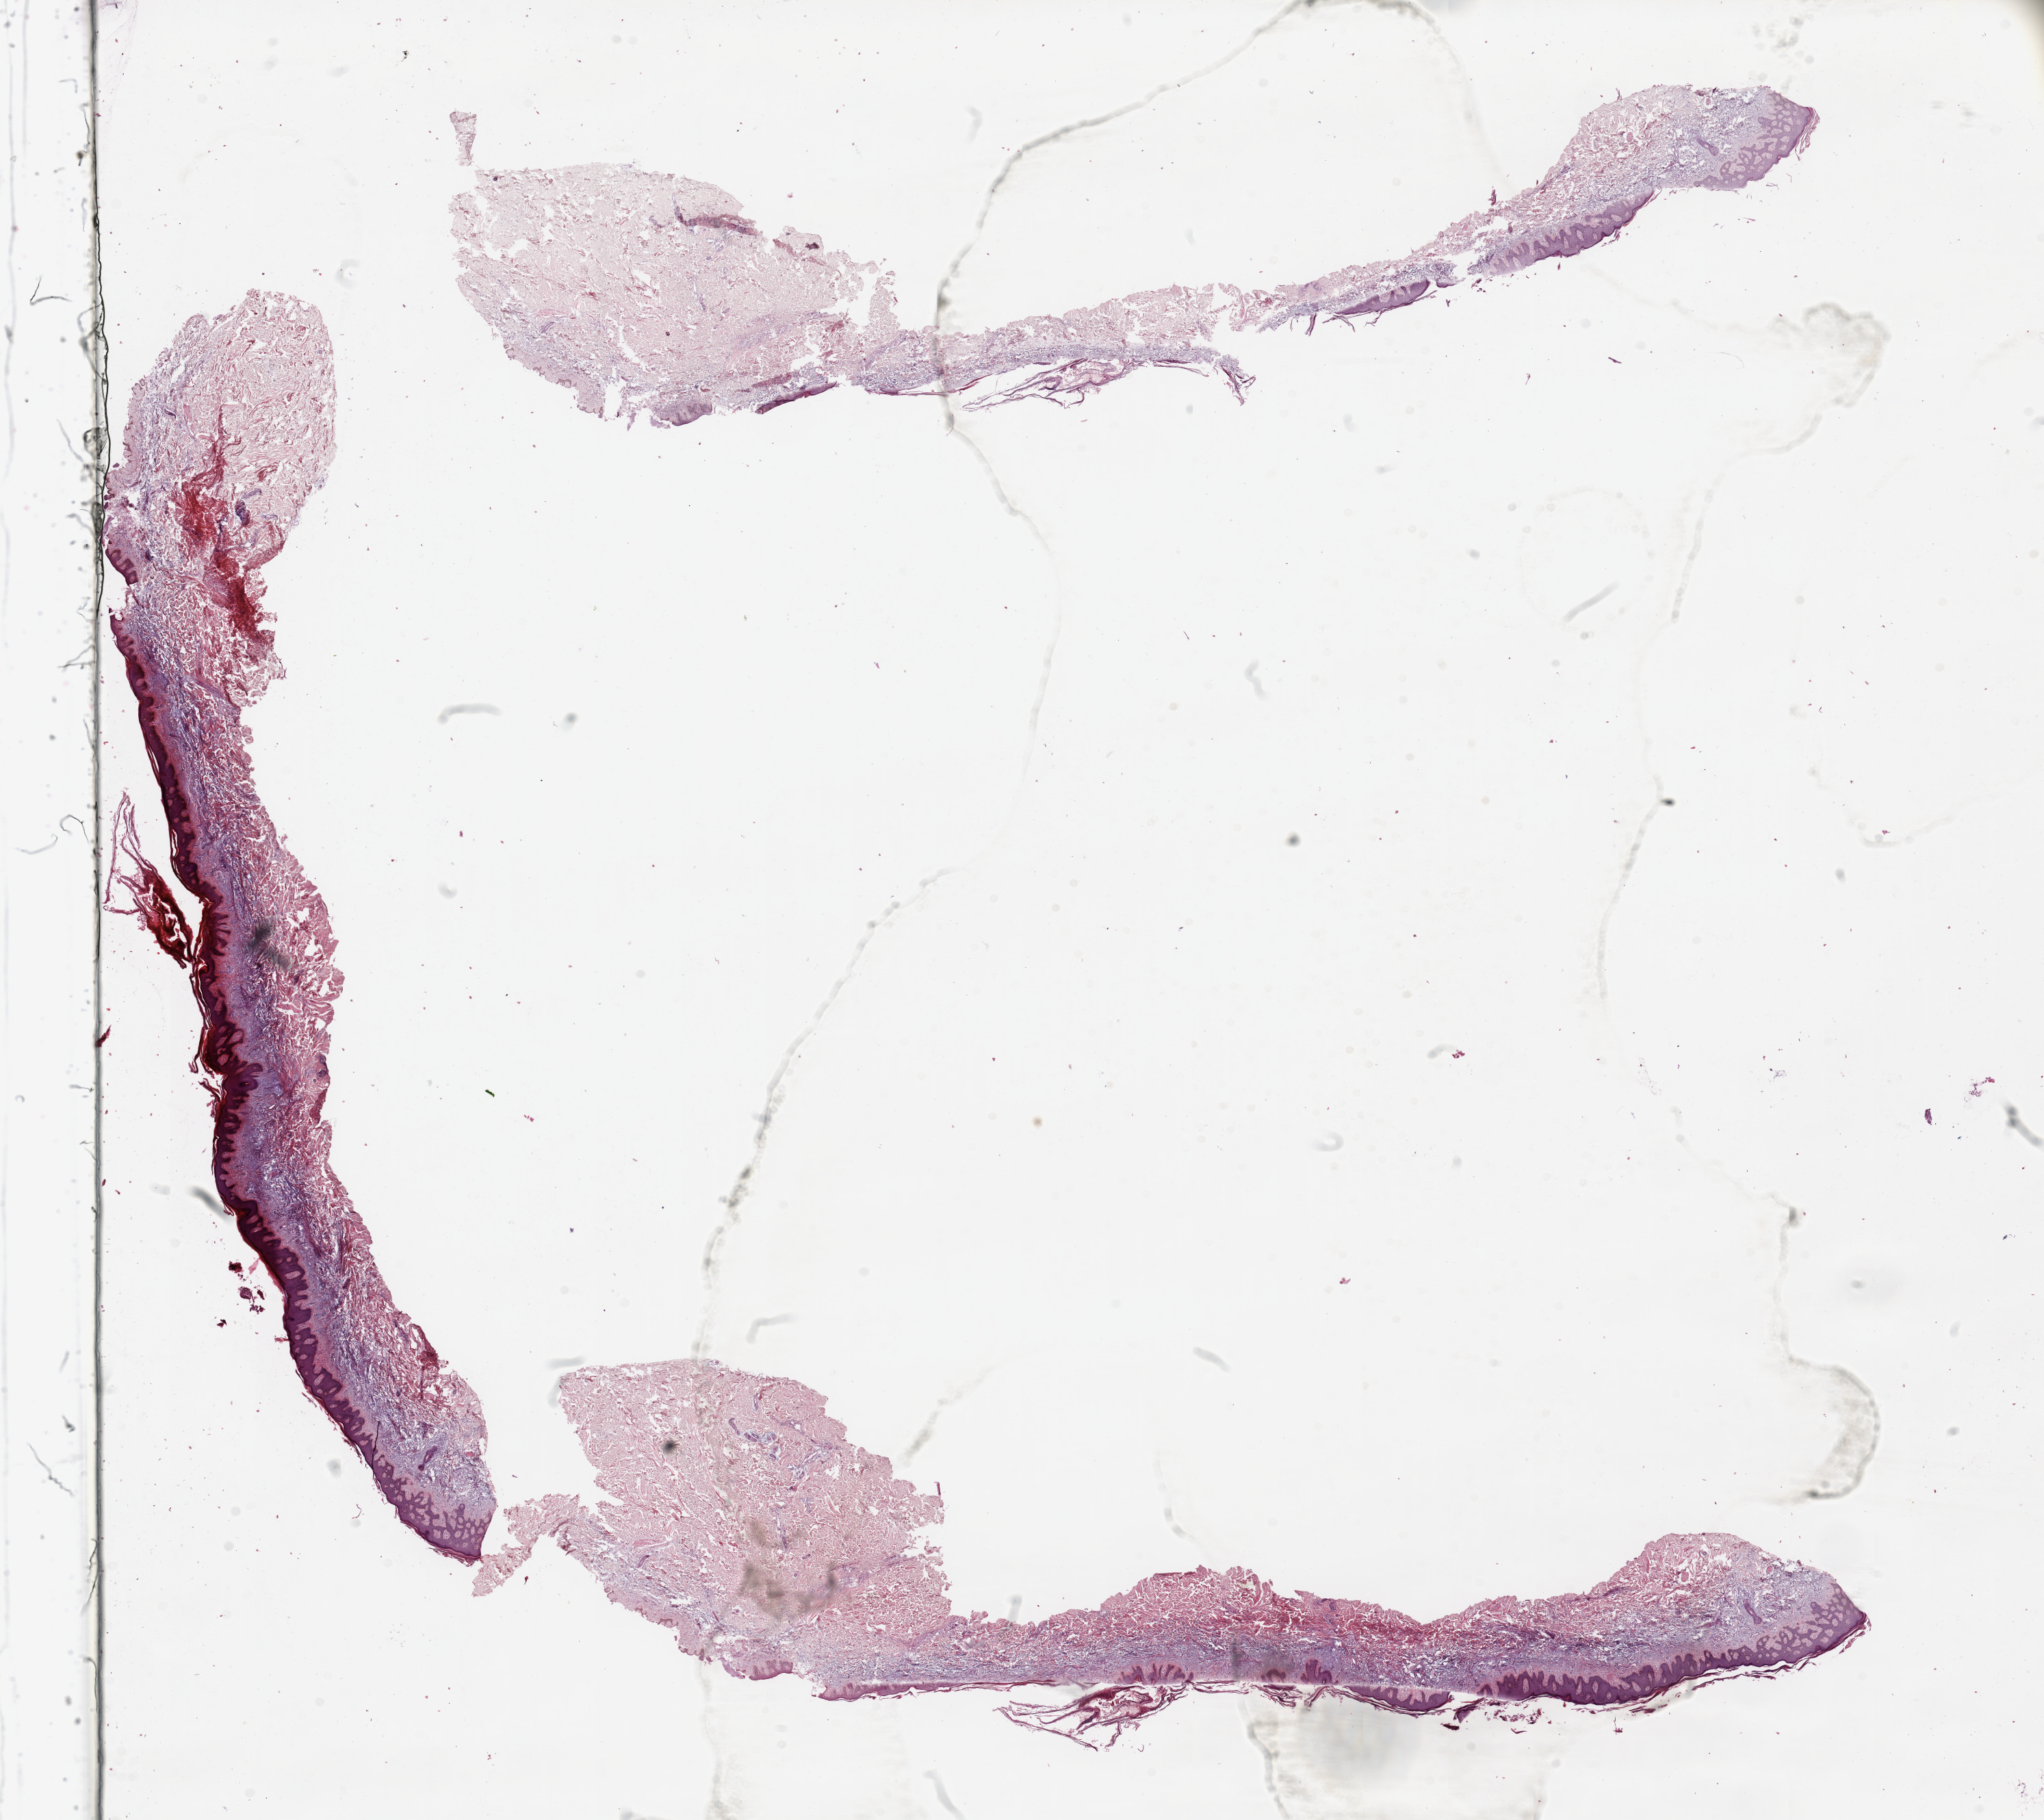
Digitized H&E tissue section (whole slide) — shown as a low-resolution overview of the whole scanned area (about 23.6 x 21.0 mm, from a 20x scan), normal (non-tumour) tissue sample, sampled site: trunk. Patient: male, age 73 years.
This section: normal (non-tumour) tissue from the same patient. Patient diagnosis: Malignant melanoma, NOS.